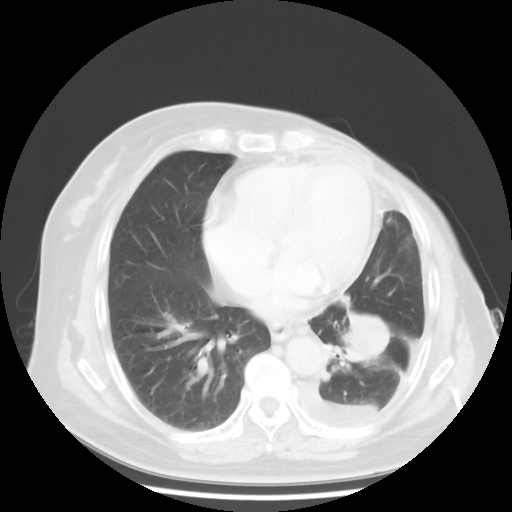
Chest CT, one axial slice; position 17 of 48 along the scan axis; 120 kVp; lung window (W 1500 / L -600 HU); 5 mm slice thickness; 512 × 512 image matrix. Patient: female, 63 years. Case-level facts recorded for this patient, not image findings: clinical TNM (as recorded): T2 N0 M1.
Annotated regions visible in this slice (rectangle marked by the reading radiologist):
- lung tumour (recorded histology: adenocarcinoma): bounding box <338,297,396,363> (left, top, right, bottom; pixels)